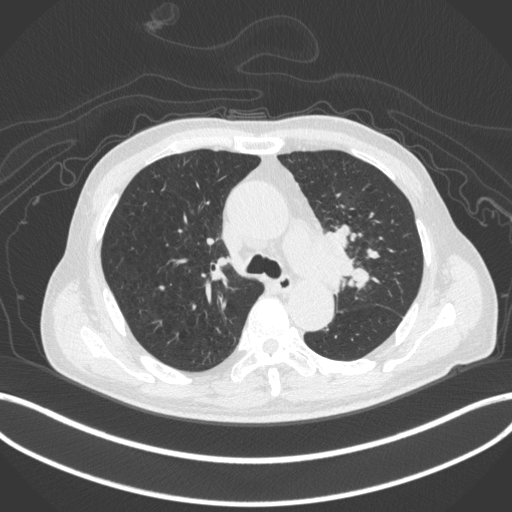
Chest CT, one axial slice. Slice 291 of 420 in the series (ordered by position). Reconstruction kernel B31f. 120 kVp. Lung window (W 1500 / L -600 HU). 1 mm slice thickness. 512 × 512 image matrix. Male patient, age 77 years. From the clinical record (not read from this slice): clinical TNM (as recorded): T3 N1 M0.
Outlined on this slice (bounding box drawn by a radiologist):
- lung tumour (recorded histology: adenocarcinoma): bounding box <298,223,363,290> (left, top, right, bottom; pixels)